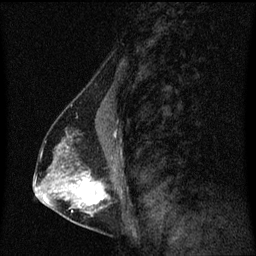
Breast MRI (dynamic contrast-enhanced), one sagittal slice. Slice 34 of 60 in the series (ordered by position). Dynamic contrast-enhanced series, image 2 of 3 at this slice position (ordered by acquisition). 1.5 T. TE 4.2 ms, TR 8.4 ms. 2 mm slice thickness. 256 × 256 image matrix, field of view 200 × 200 mm. Patient: female, 40 years. From the clinical record (not read from this slice): setting: breast cancer imaged before/during neoadjuvant chemotherapy; receptor status: triple-negative.
Annotated regions visible in this slice (semi-automatic segmentation, software-assisted and operator-edited):
- analysis volume of interest (the breast-tissue region the enhancement analysis was run in; not a lesion): box from (x=44, y=128) to (x=117, y=221) px
- tumour enhancement mask (voxels above the 70 % enhancement threshold inside the analysis volume of interest): (x=78, y=174)–(x=107, y=207)